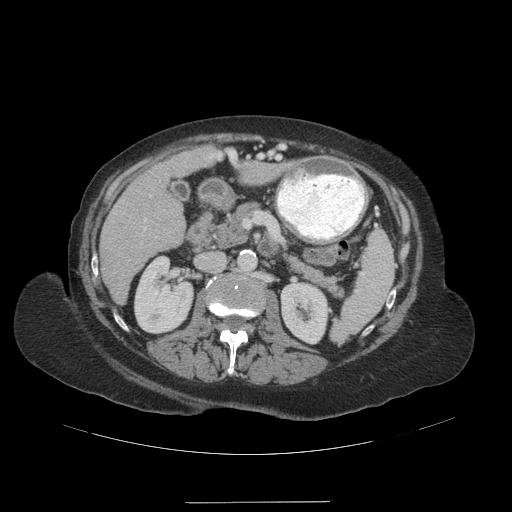
Contrast-enhanced abdominal CT (liver protocol), one axial slice; slice 50 of 99 in the series (ordered by position); 140 kVp; soft-tissue window (W 400 / L 40 HU); 2.5 mm slice thickness; 512 × 512 image matrix, field of view 440 × 440 mm. Case-level facts recorded for this patient, not image findings: diagnosis: hepatocellular carcinoma (patient treated with transarterial chemoembolisation; whether this scan precedes or follows treatment is not stated here); TNM stage (as recorded): Stage-IVA; Child-Pugh class: A.
Annotated regions visible in this slice (semi-automatically segmented with operator editing):
- liver parenchyma outside the tumour (the mass and vessels are separate outlines, so this box may not span the whole liver): box from (x=100, y=146) to (x=221, y=302) px
- liver vessels: (x=144, y=153)–(x=221, y=230)